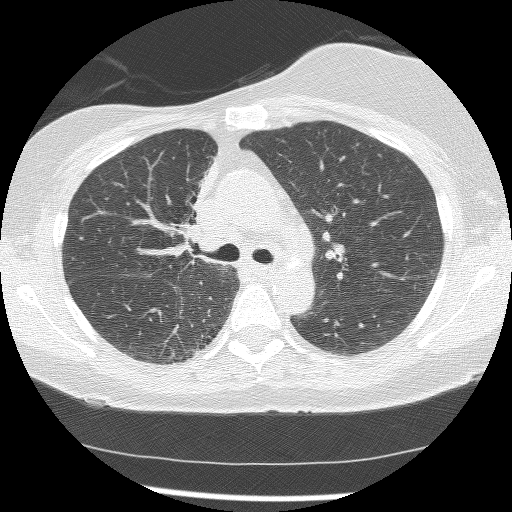
Low-dose screening chest CT, axial slice; baseline annual screen; lung window (W 1500 / L -600 HU); 2.5 mm slice thickness; lung (sharp) reconstruction kernel (BONE). Female participant, aged 56 years at enrolment.
Lesion marked by an expert reader, box from (x=162, y=161) to (x=218, y=262) px. The screening reader recorded 2 non-calcified nodules or masses ≥4 mm on this exam (right lower lobe, right middle lobe); which of them this box marks is not recorded.